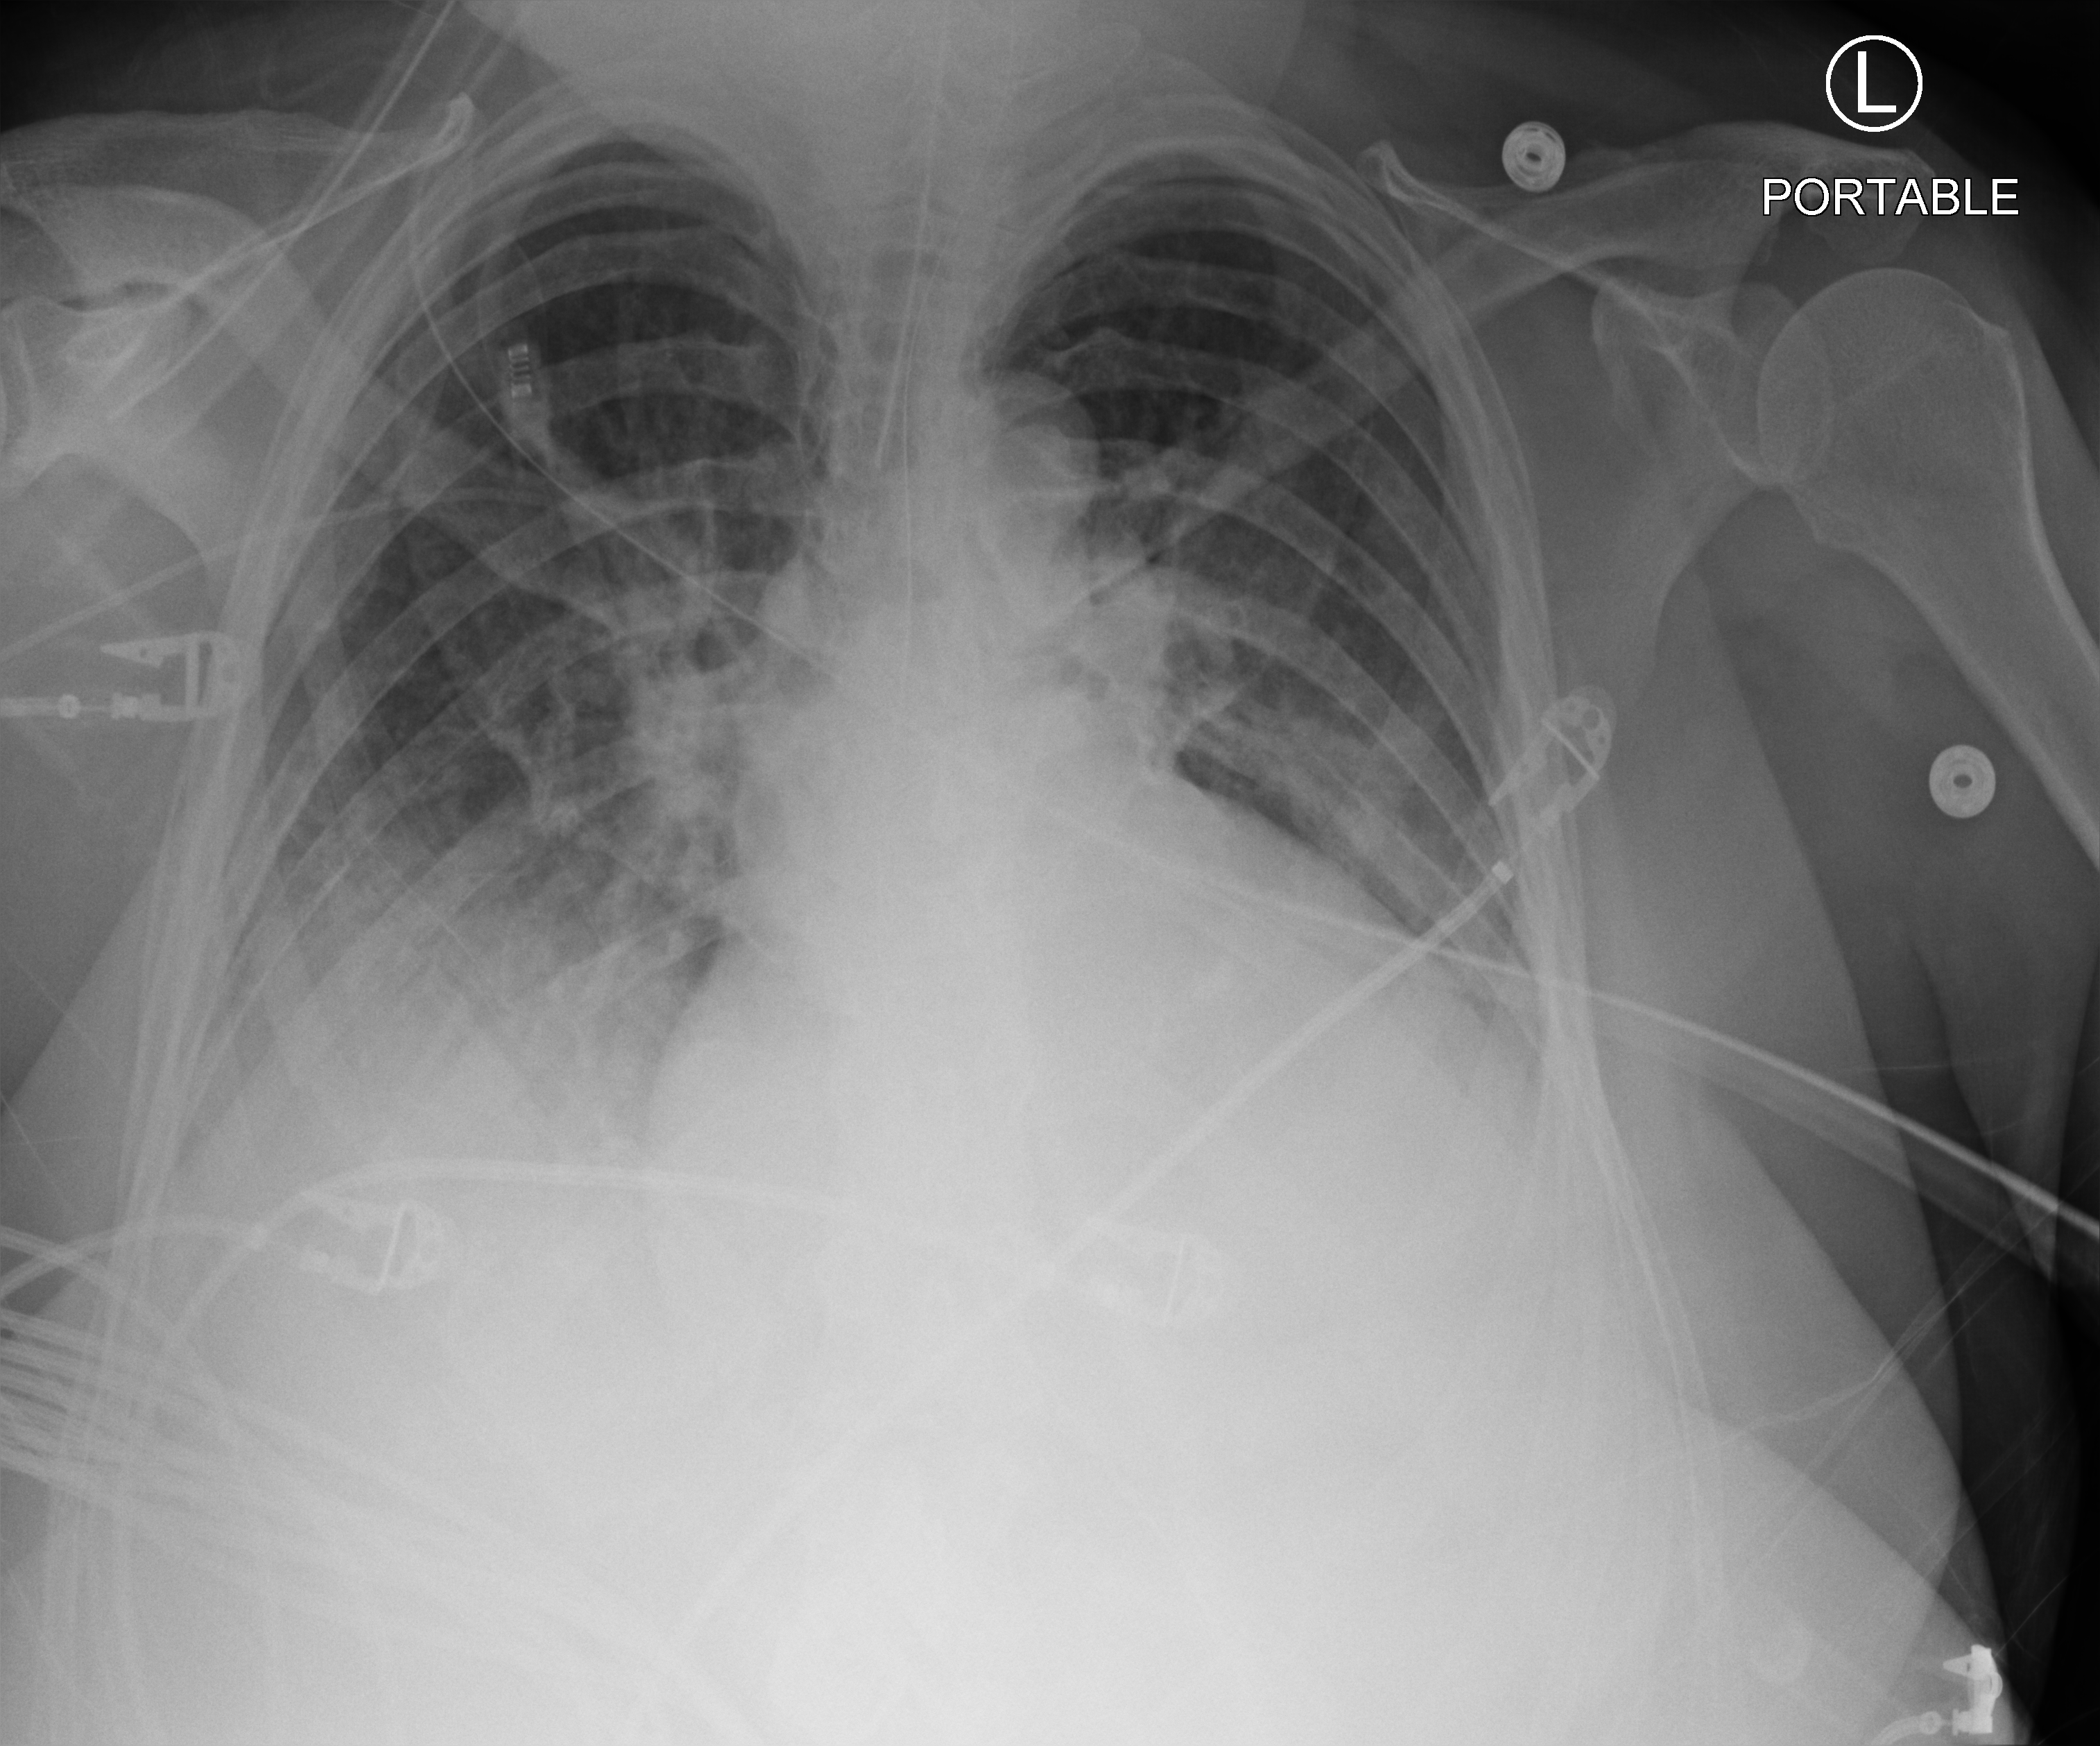
Portable chest radiograph. Patient hospitalised with COVID-19; female, aged 60–74 years.
Admission-level facts for this patient (not findings on this image; timing relative to this image not recorded): mechanically ventilated during this hospital stay: yes; length of hospital stay: 50 days; admitted to intensive care during this hospital stay: yes.